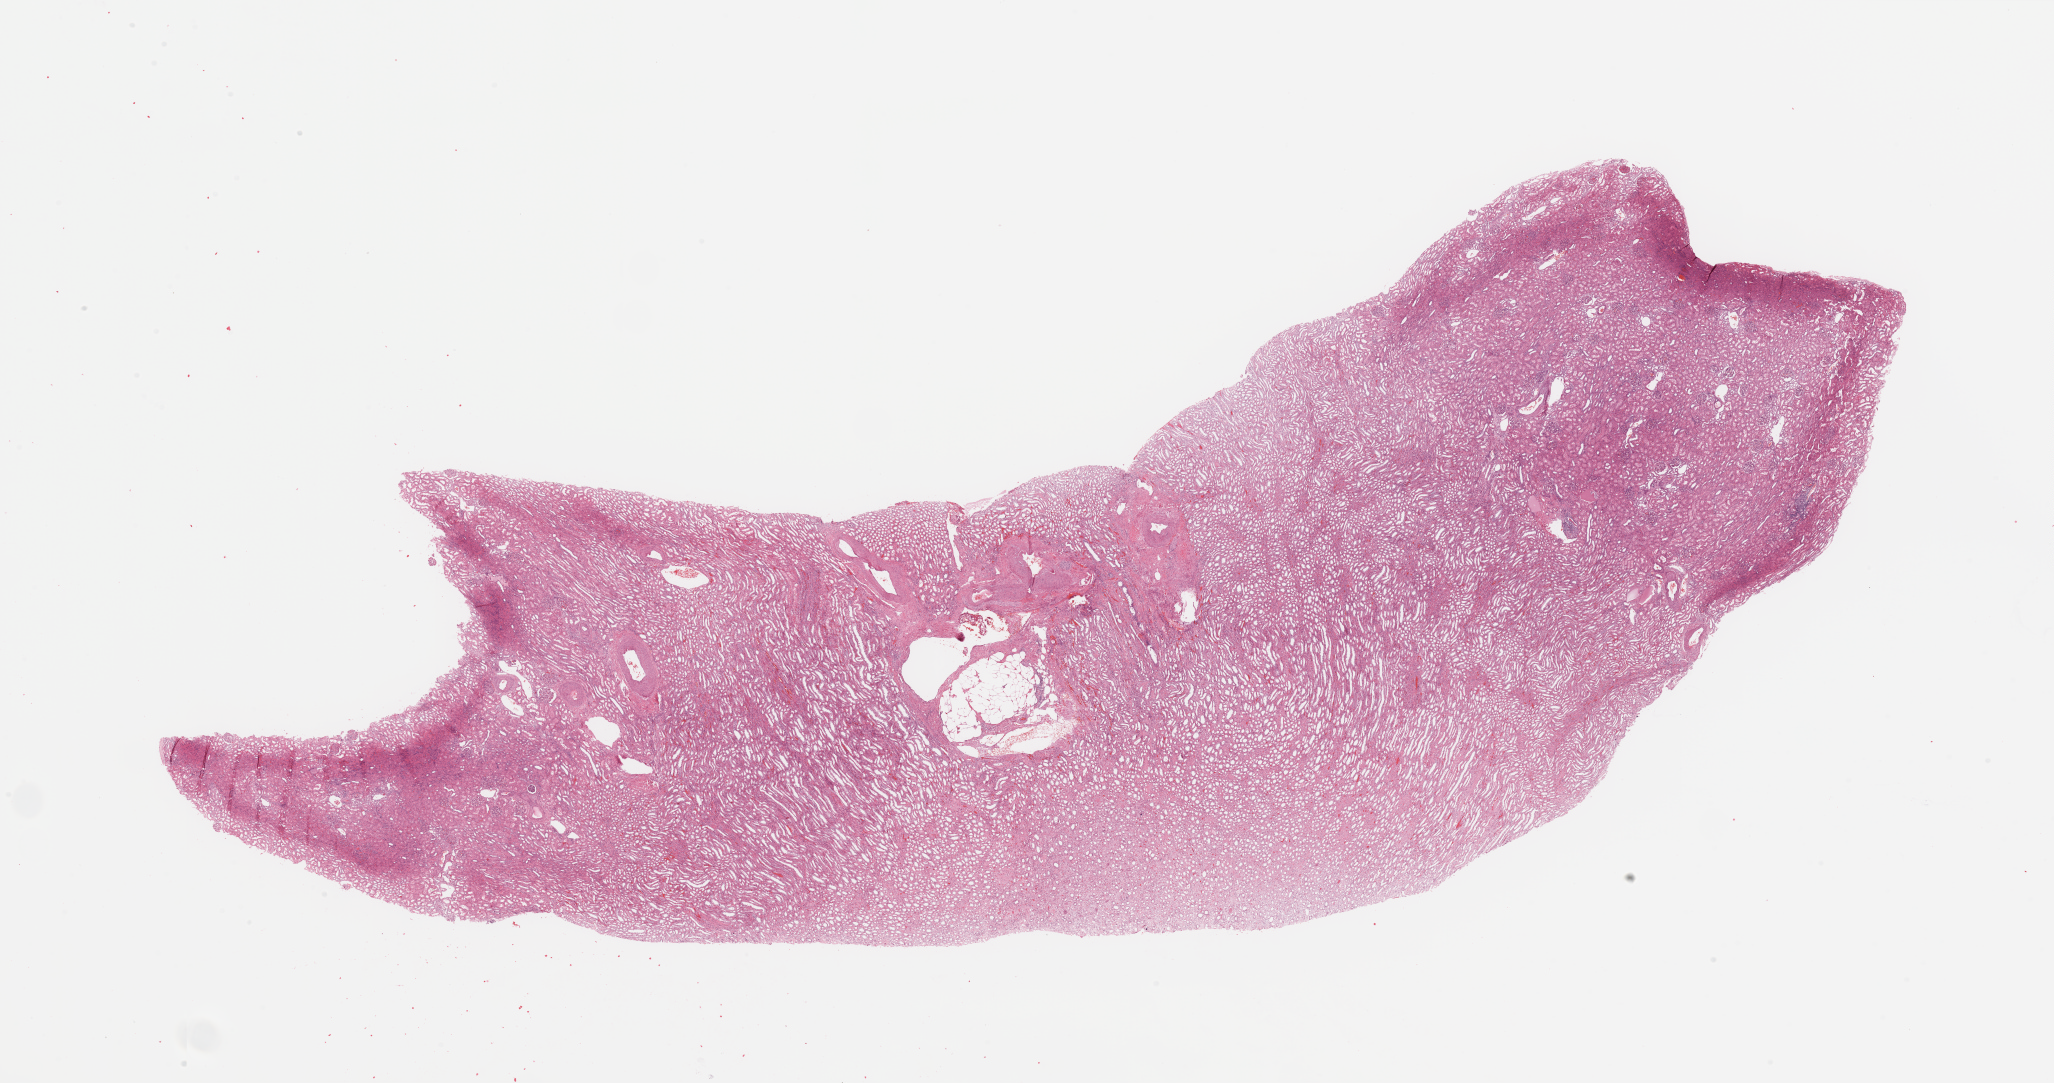
Hematoxylin and eosin (H&E) stained whole-slide image — a low-resolution overview of the entire scanned area, about 32.5 x 17.1 mm. Kidney, normal (non-tumour) tissue. 61-year-old male patient.
This section: normal (non-tumour) tissue from the same patient. Patient diagnosis: Renal cell carcinoma, NOS.